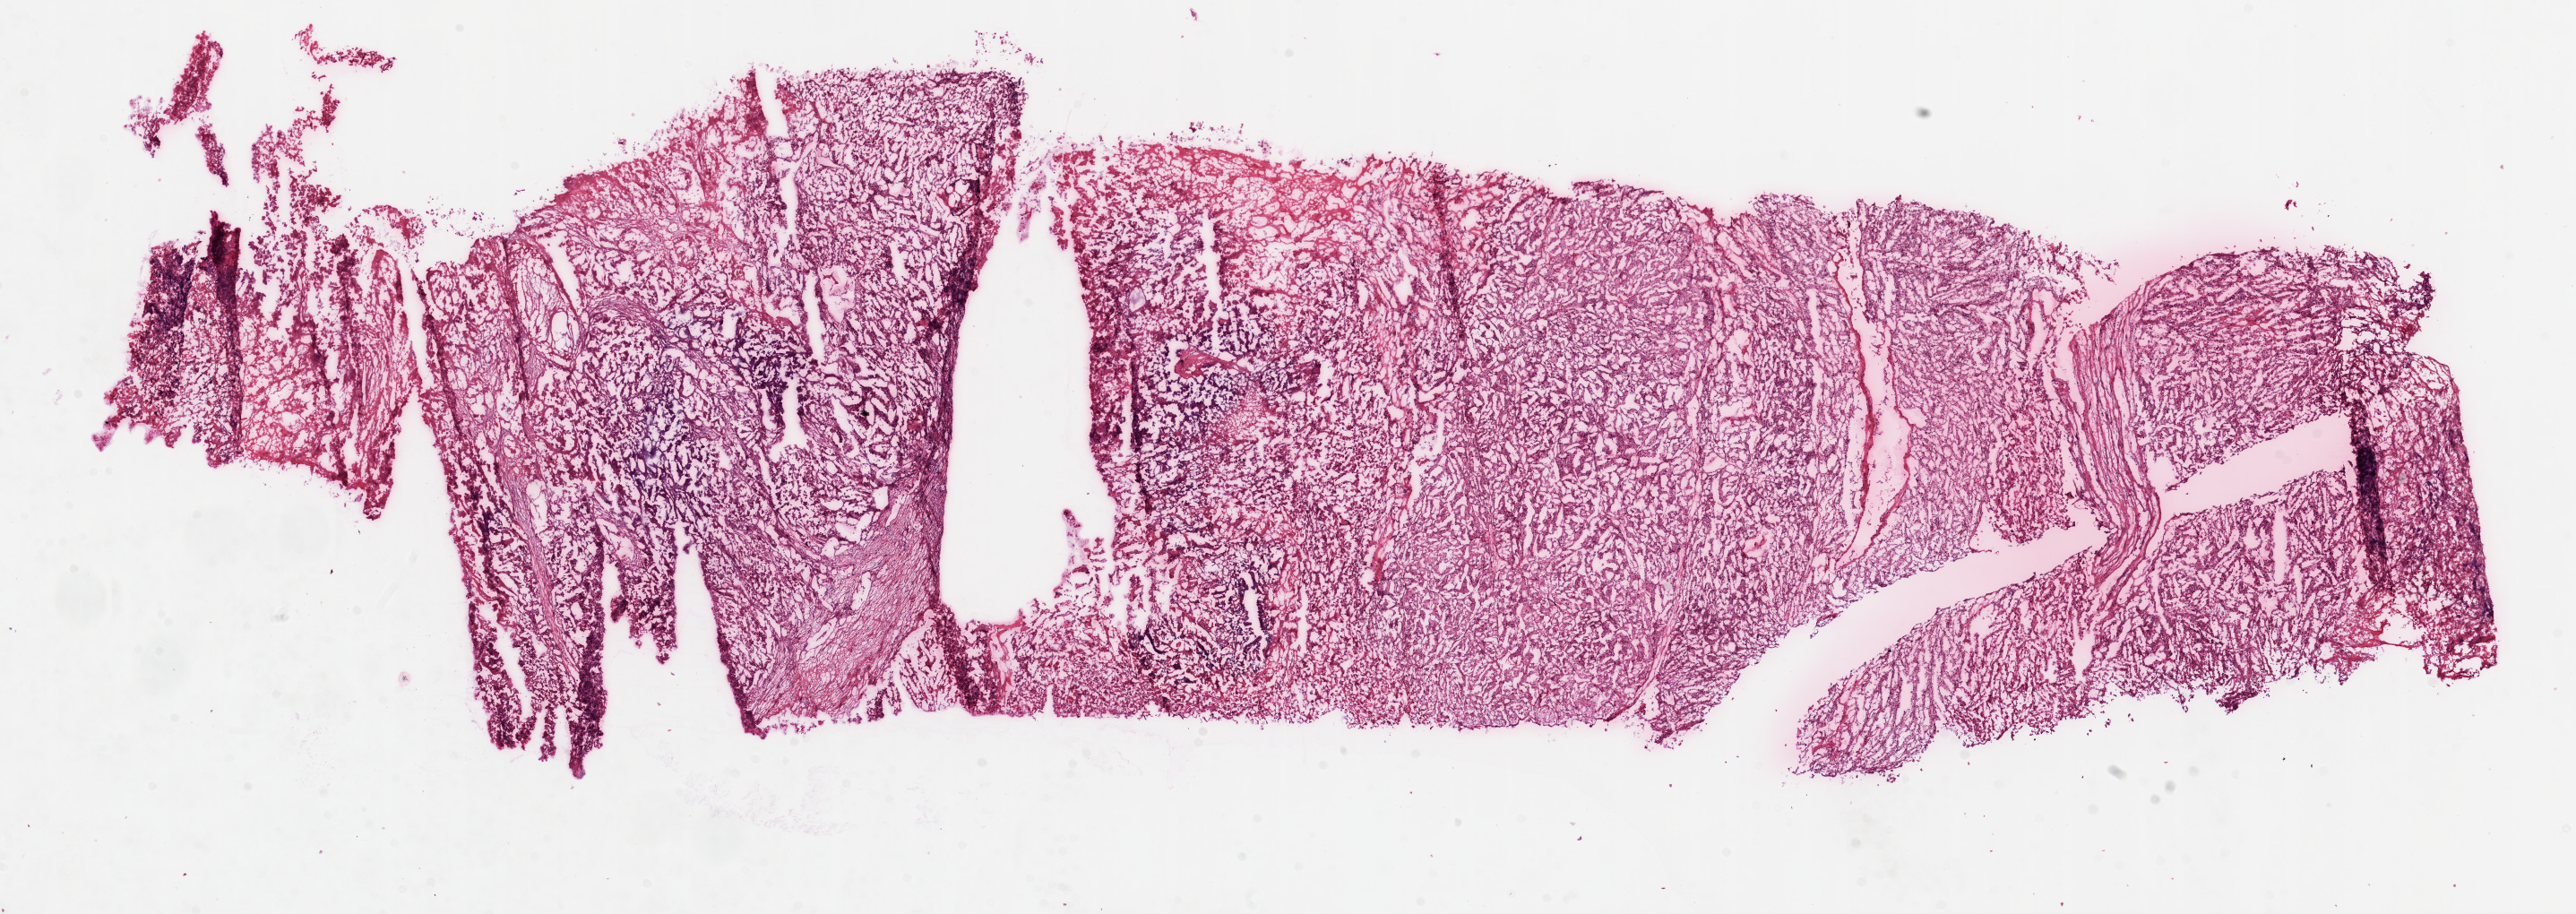
H&E-stained whole-slide image — a low-resolution overview of the entire scanned area, about 23.1 x 8.2 mm (from a 20x scan); frozen section from the top of the tissue portion; sample: primary tumour, kidney. Patient: female, age at initial diagnosis 45 years. Histologic grade: G4 (undifferentiated). Pathologist review of this section (percent, as recorded): tumour cells 95%, tumour nuclei 85%, normal cells 0%, stromal cells 5%, necrosis 0%.
• laterality: left
• AJCC pathologic stage: III
• diagnosis: Clear cell adenocarcinoma, NOS